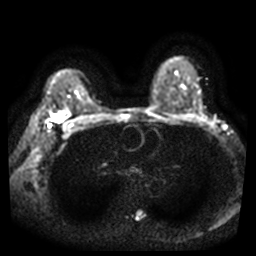
Breast MRI, one axial slice. Slice 29 of 44 in the series (ordered by position). Diffusion-weighted series; image 2 of 4 stored at this slice position (different b-values; order by instance number). 3 T. 5 mm slice thickness. 256 × 256 image matrix, field of view 340 × 340 mm. Female patient.
Structures marked on this image (manually delineated by an expert):
- tumour on diffusion-weighted imaging: box from (x=52, y=115) to (x=58, y=121) px